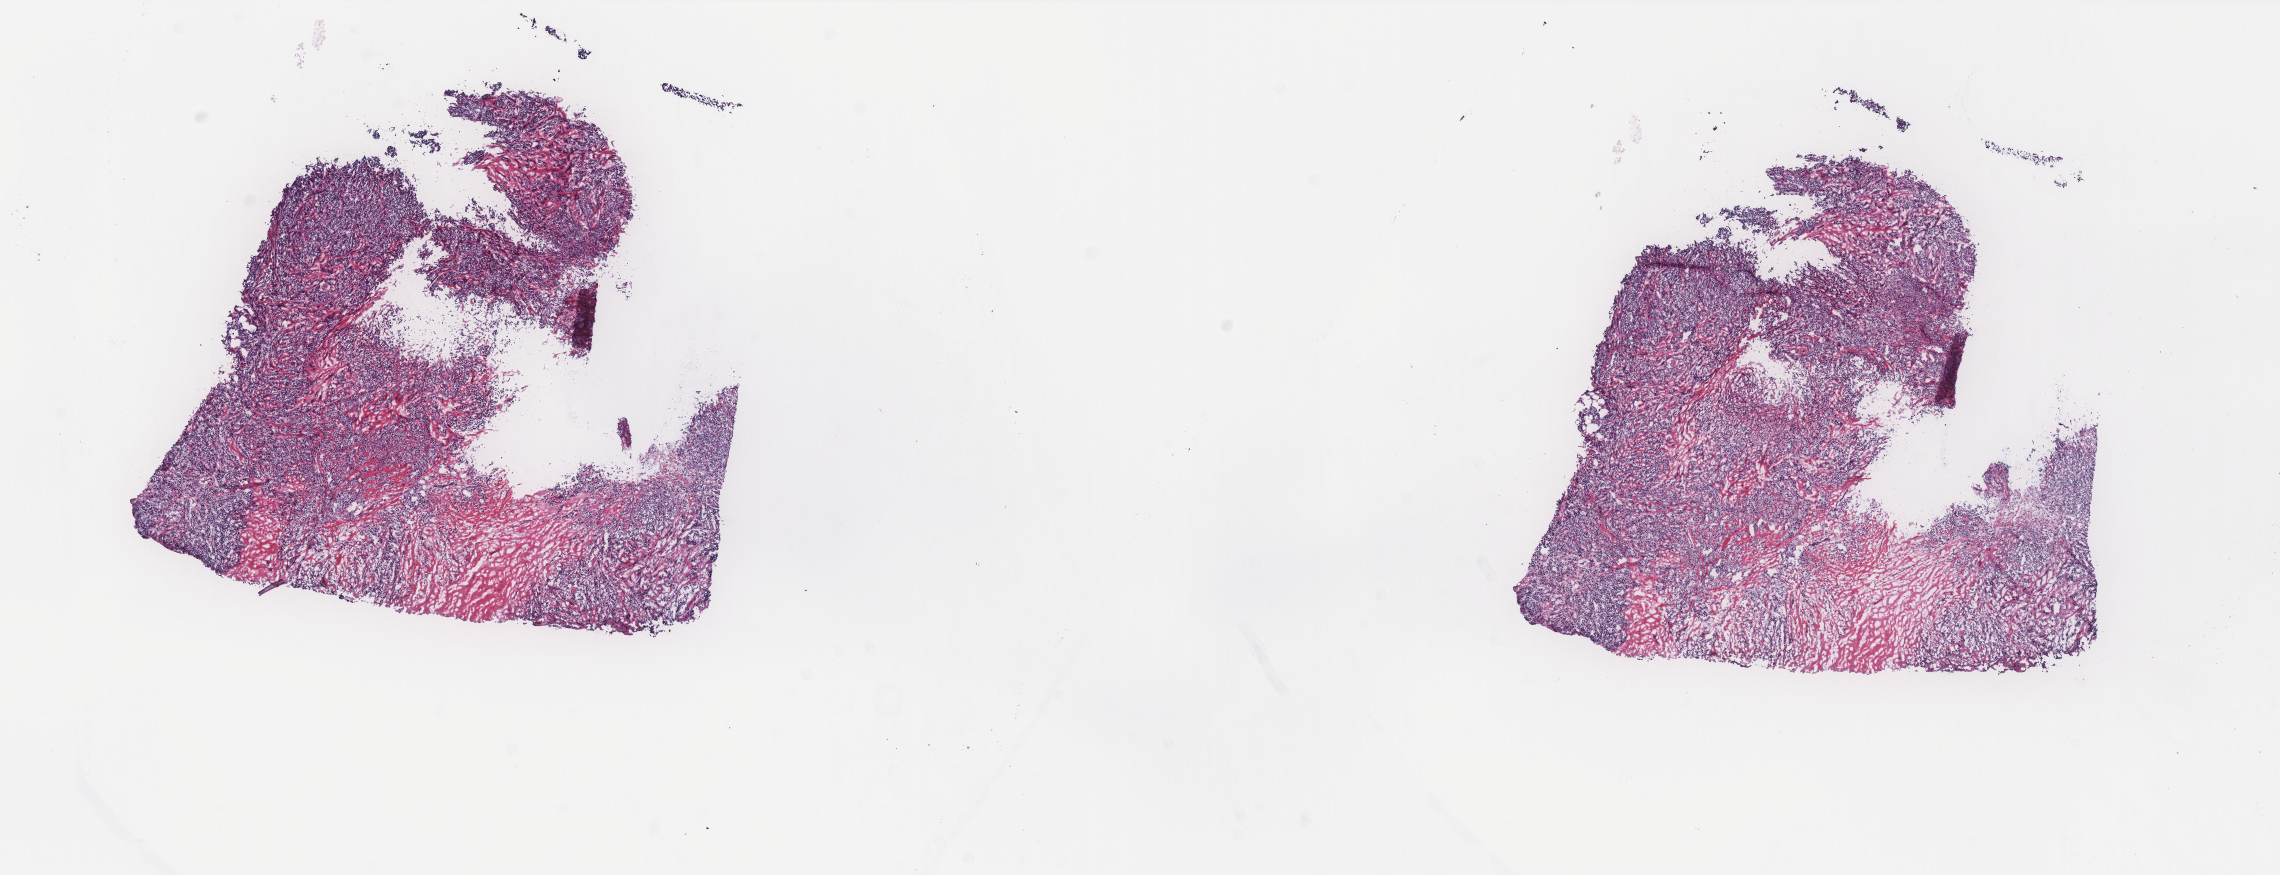
Whole-slide histology image, Hematoxylin and eosin (H&E) stained — whole scanned area (about 18.3 x 7.0 mm) shown as a low-resolution overview; frozen section from the top of the tissue portion; primary tumour sample from the breast. Patient: female, age at initial diagnosis 80 years. Pathologist review of this section (percent, as recorded): tumour cells 80%, tumour nuclei 80%, normal cells 0%, stromal cells 20%, necrosis 0%. Inflammatory infiltration, as recorded: lymphocyte infiltration 3%, monocyte infiltration 1%, neutrophil infiltration 0%.
Pathologic diagnosis: Lobular carcinoma, NOS. TNM: T3 N3a MX. AJCC pathologic stage: IIIC (7th edition).